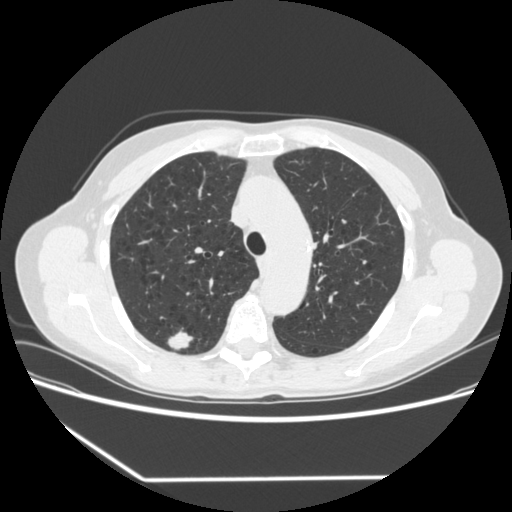
Chest CT (low-dose screening protocol), one axial image, baseline screening round, lung window (W 1500 / L -600 HU), 1.25 mm slice thickness, standard (soft-tissue) reconstruction kernel (STANDARD), slice 245 of 323 in the series. Female, age 67 years at enrolment.
Expert reader's lesion annotation, bounding box [x1, y1, x2, y2] px = [155, 323, 200, 358]. The screening reader recorded 2 non-calcified nodules or masses ≥4 mm on this exam (right upper lobe, right lower lobe); which of them this box marks is not recorded. Official screen result: positive, change unspecified: nodule(s) >= 4 mm or enlarging nodule(s), mass(es), or other non-specific abnormalities suspicious for lung cancer. Lung cancer was diagnosed 29 days after this screen: adenocarcinoma, NOS, right upper lobe, moderately differentiated (G2), stage IA (AJCC 6th edition), 24 mm at pathology.